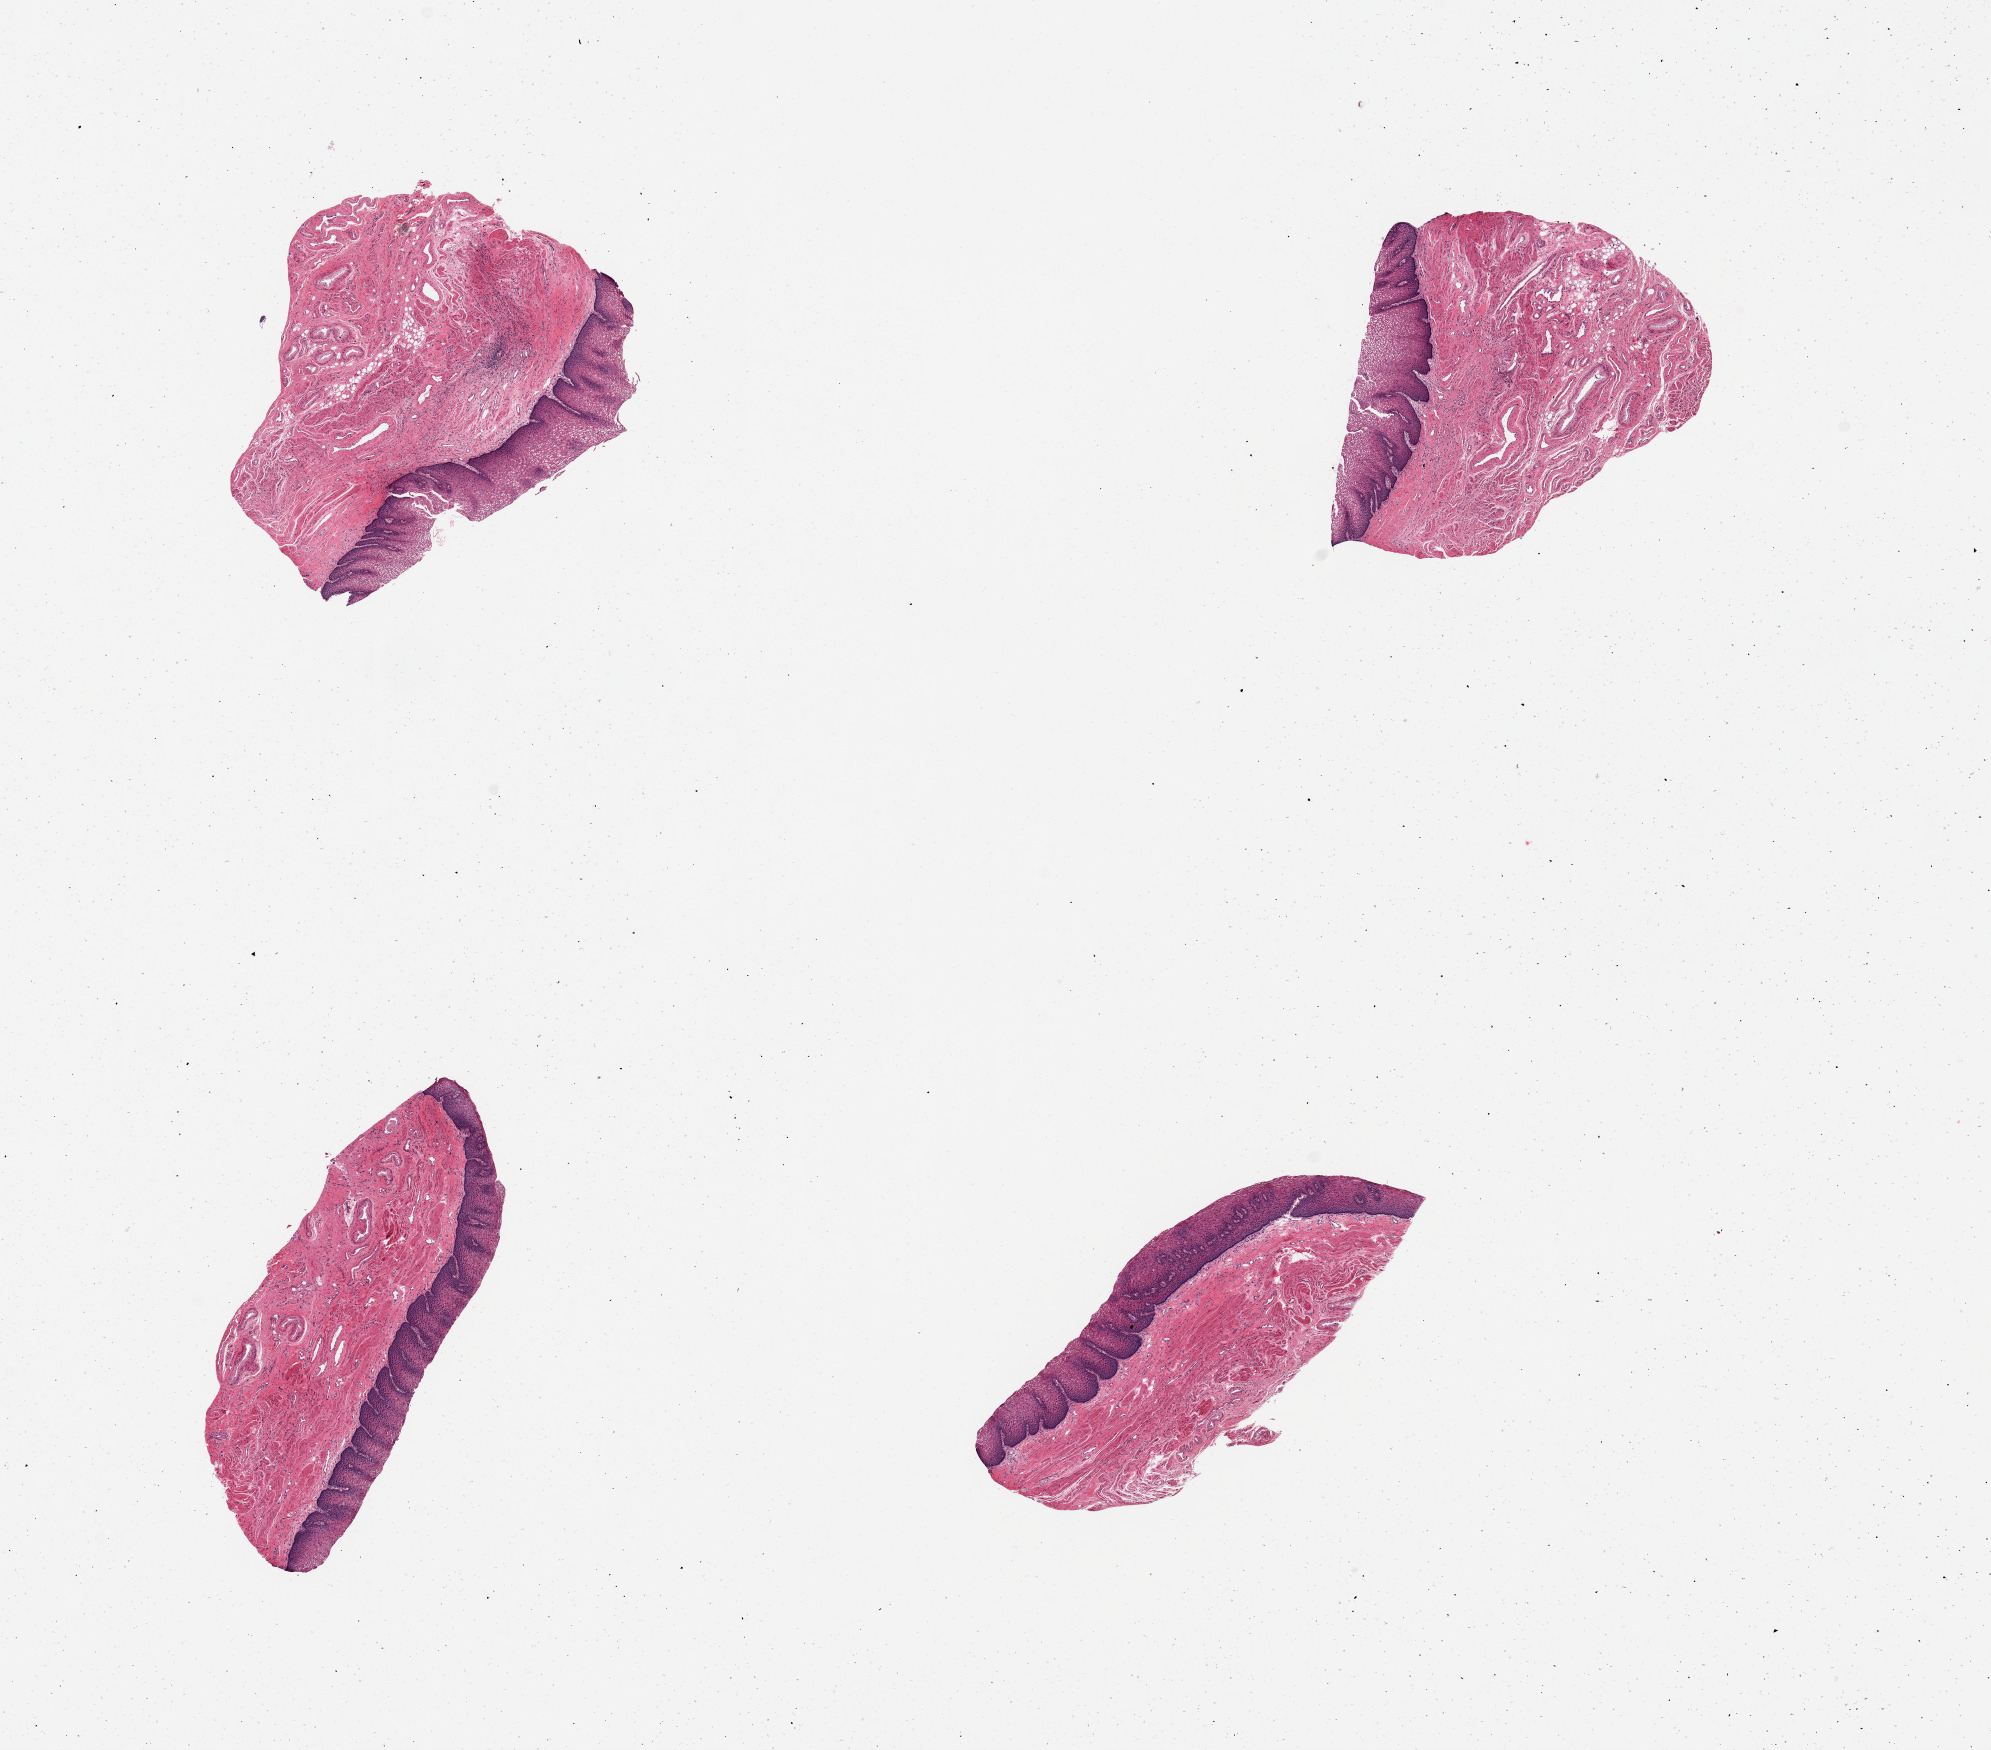
Digitized hematoxylin and eosin (H&E)-stained section — shown as a low-resolution overview of the whole scanned area (about 15.8 x 13.8 mm); PAXgene-fixed paraffin-embedded (PFPE) section; target tissue: gastroesophageal junction; tissue donor sample. Donor sex: male.
* pathologist's review note for this sample: 4 pieces; squamous mucosa, not muscularis